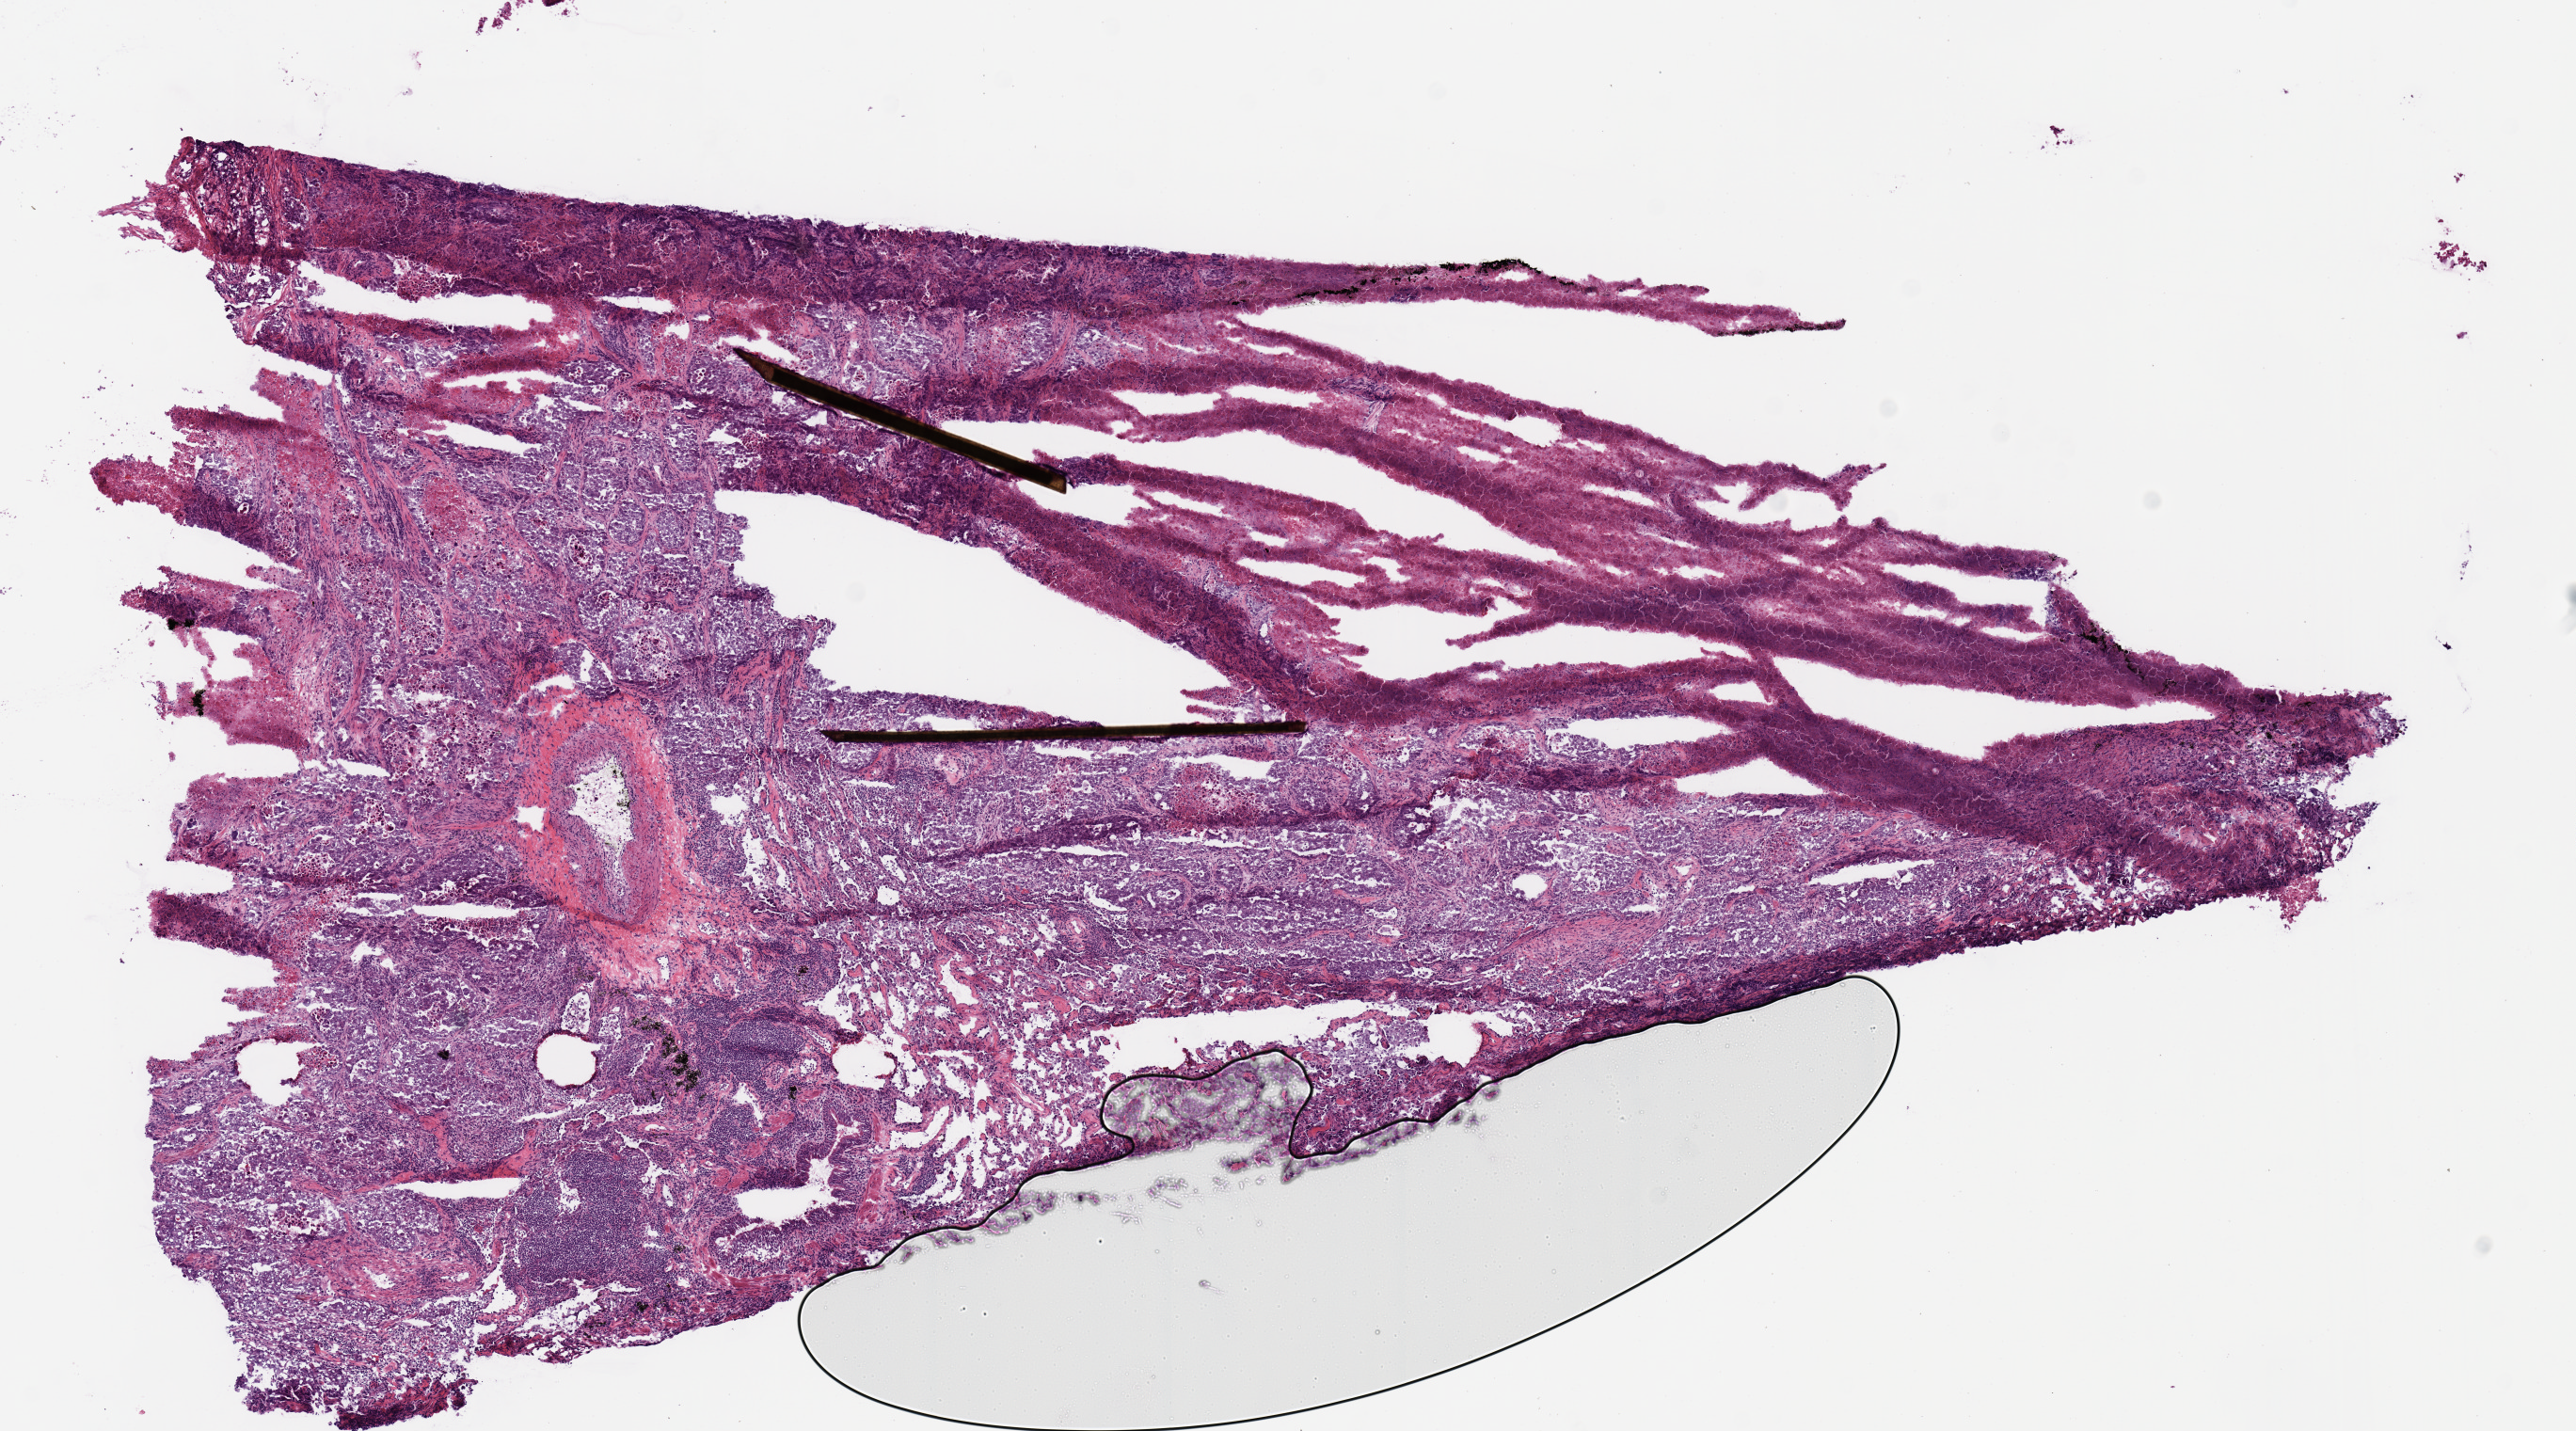
Whole-slide histology image, H&E, shown as a low-resolution overview of the whole scanned area (about 10.8 x 6.0 mm); frozen section from the top of the tissue portion; lung, primary tumour sample. Patient: male, age at initial diagnosis 69 years. Slide review estimates, as recorded: tumour cells 90%, tumour nuclei 70%, normal cells 0%, stromal cells 10%, necrosis 0%.
- AJCC pathologic stage: IIB (6th edition)
- histologic diagnosis: Adenocarcinoma, NOS (lower lobe, lung)